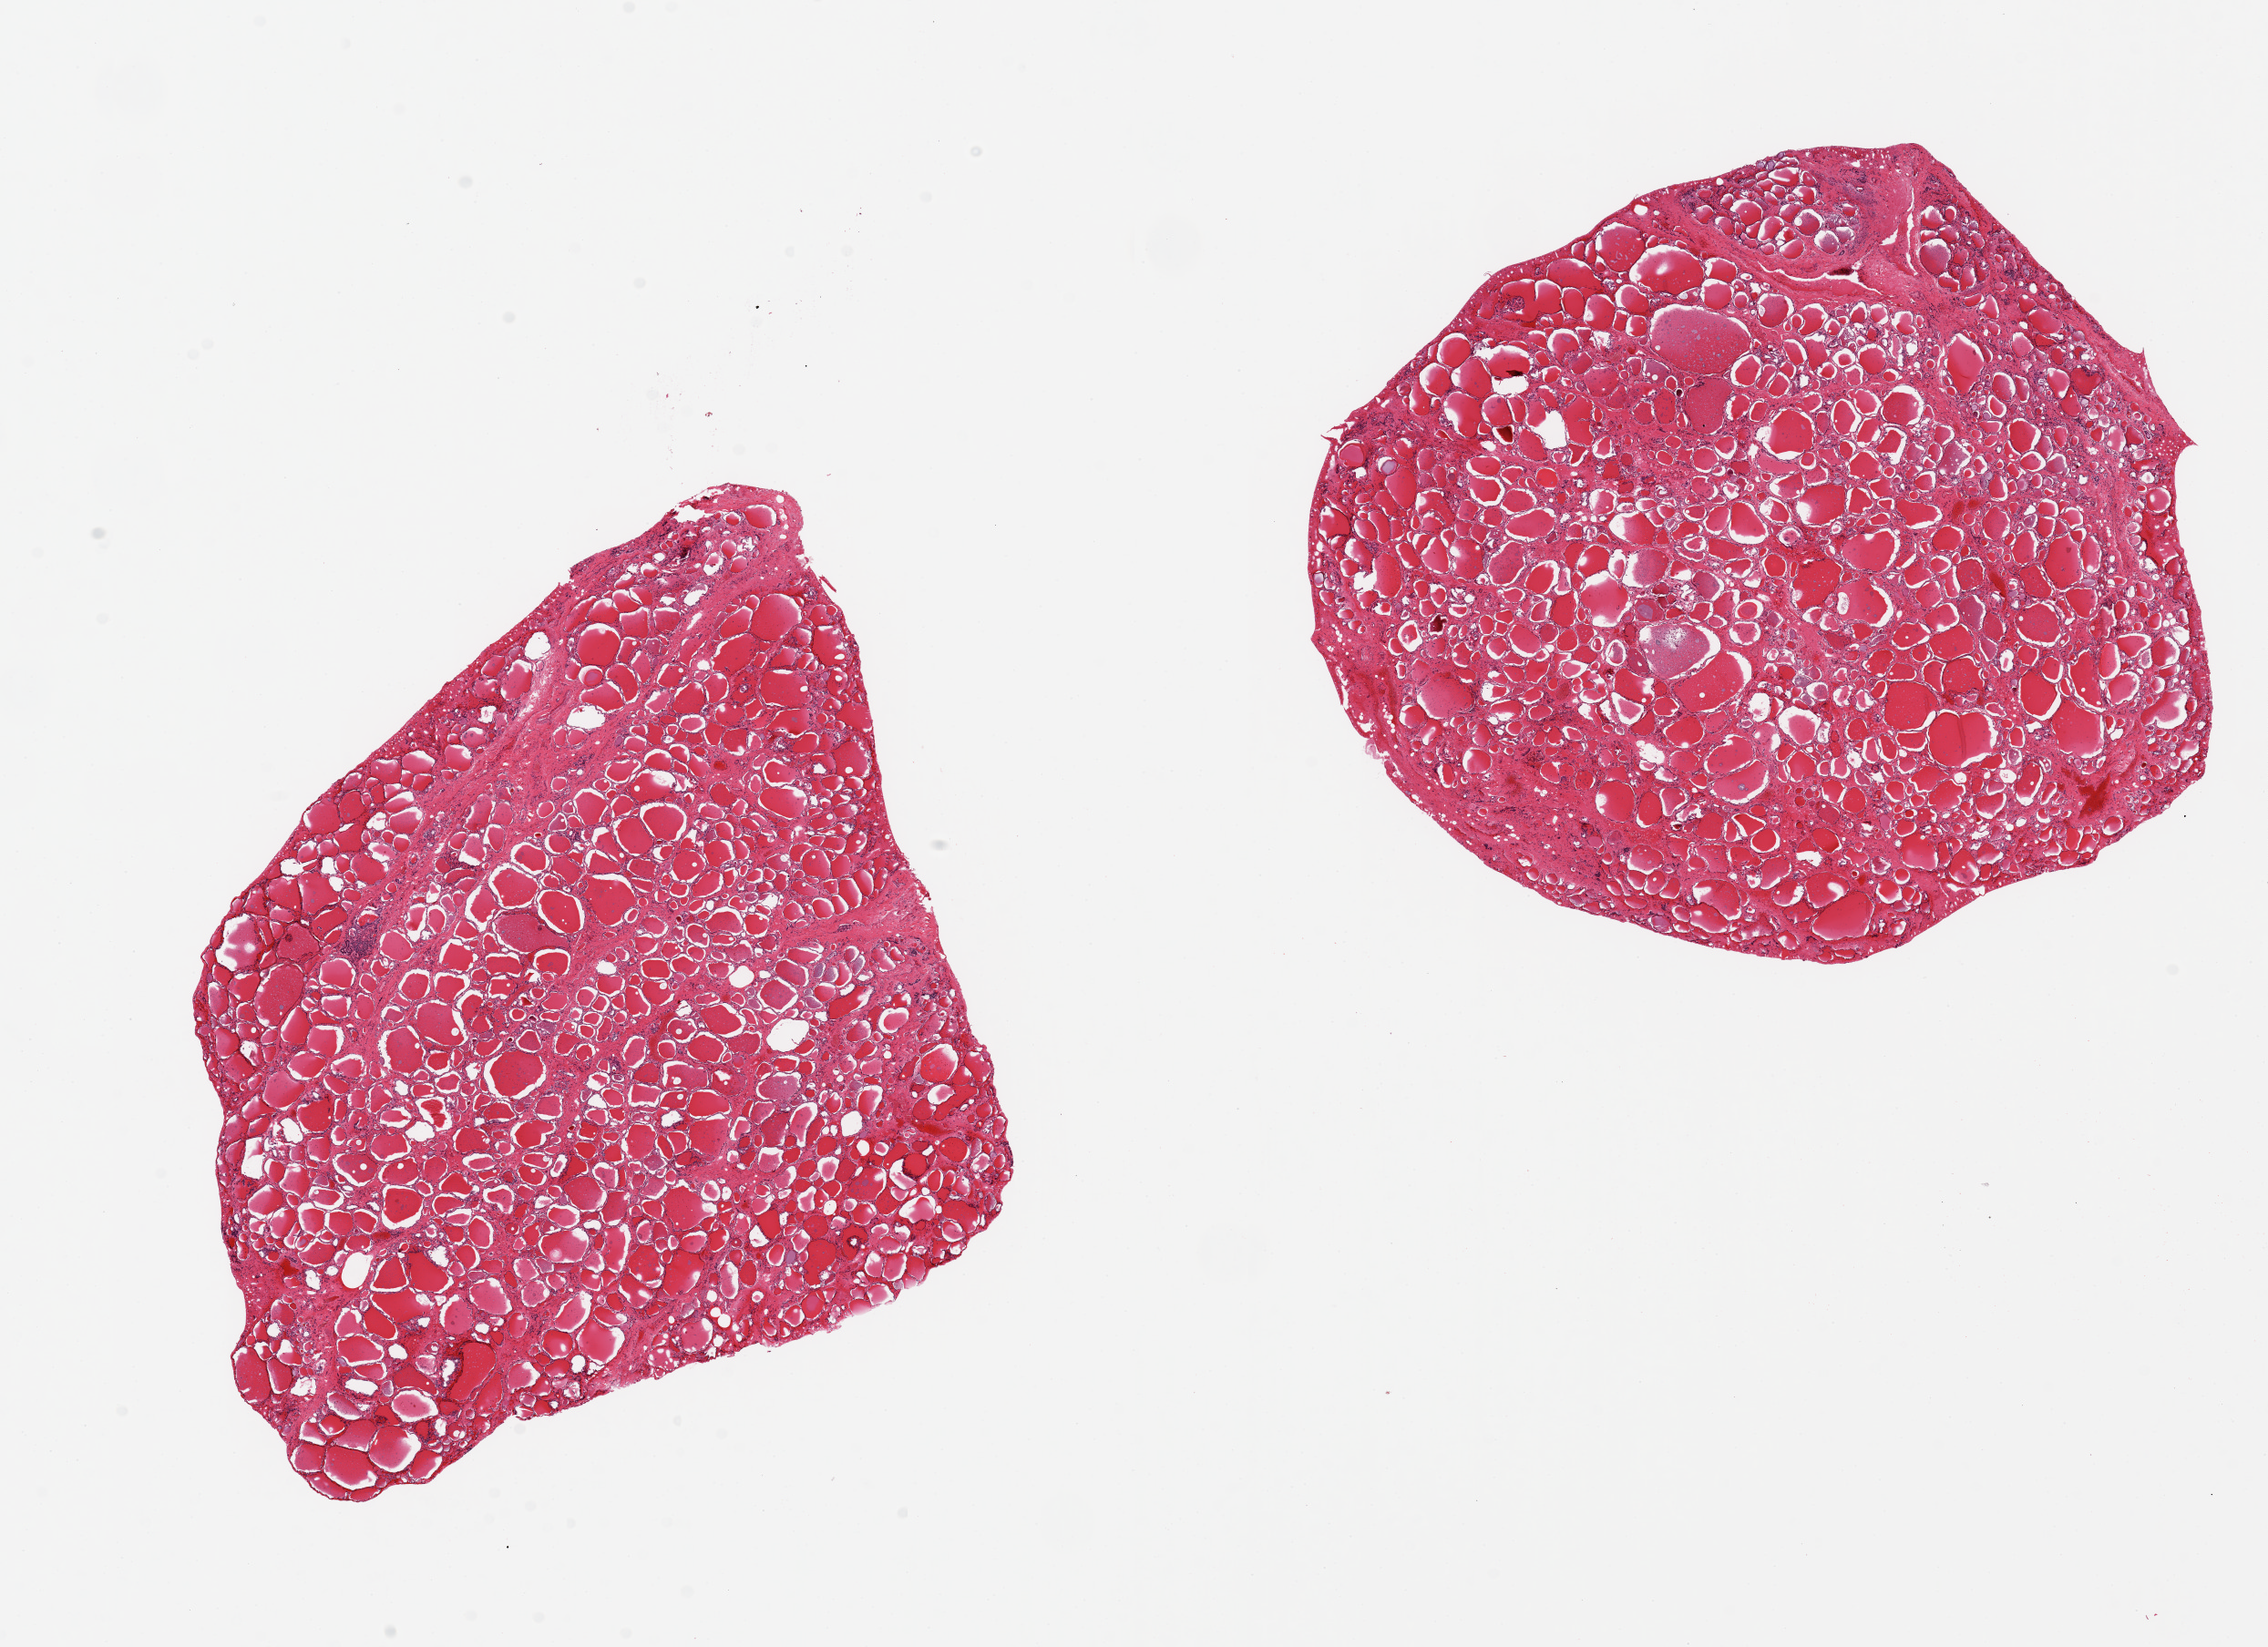
Whole-slide image, H&E stain — shown as a low-resolution overview of the whole scanned area (about 19.7 x 14.3 mm); PAXgene-fixed, paraffin-embedded tissue; target tissue: thyroid; tissue donor sample. Donor: female.
Review note (as recorded): 2pieces ~ 7x7mm, unusually poorly preserved.